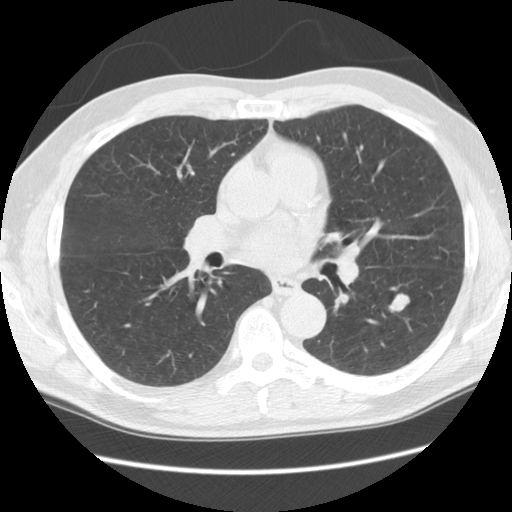
Low-dose screening chest CT, one axial slice; slice 56 of 111 in the series (ordered by position); reconstruction kernel STANDARD; lung window (W 1500 / L -600 HU); 512 × 512 image matrix, field of view 370 × 370 mm.
Annotated regions visible in this slice (manually delineated by an expert):
- lesion 1 (tumor, lower lobe of left lung): box from (x=389, y=293) to (x=409, y=312) px